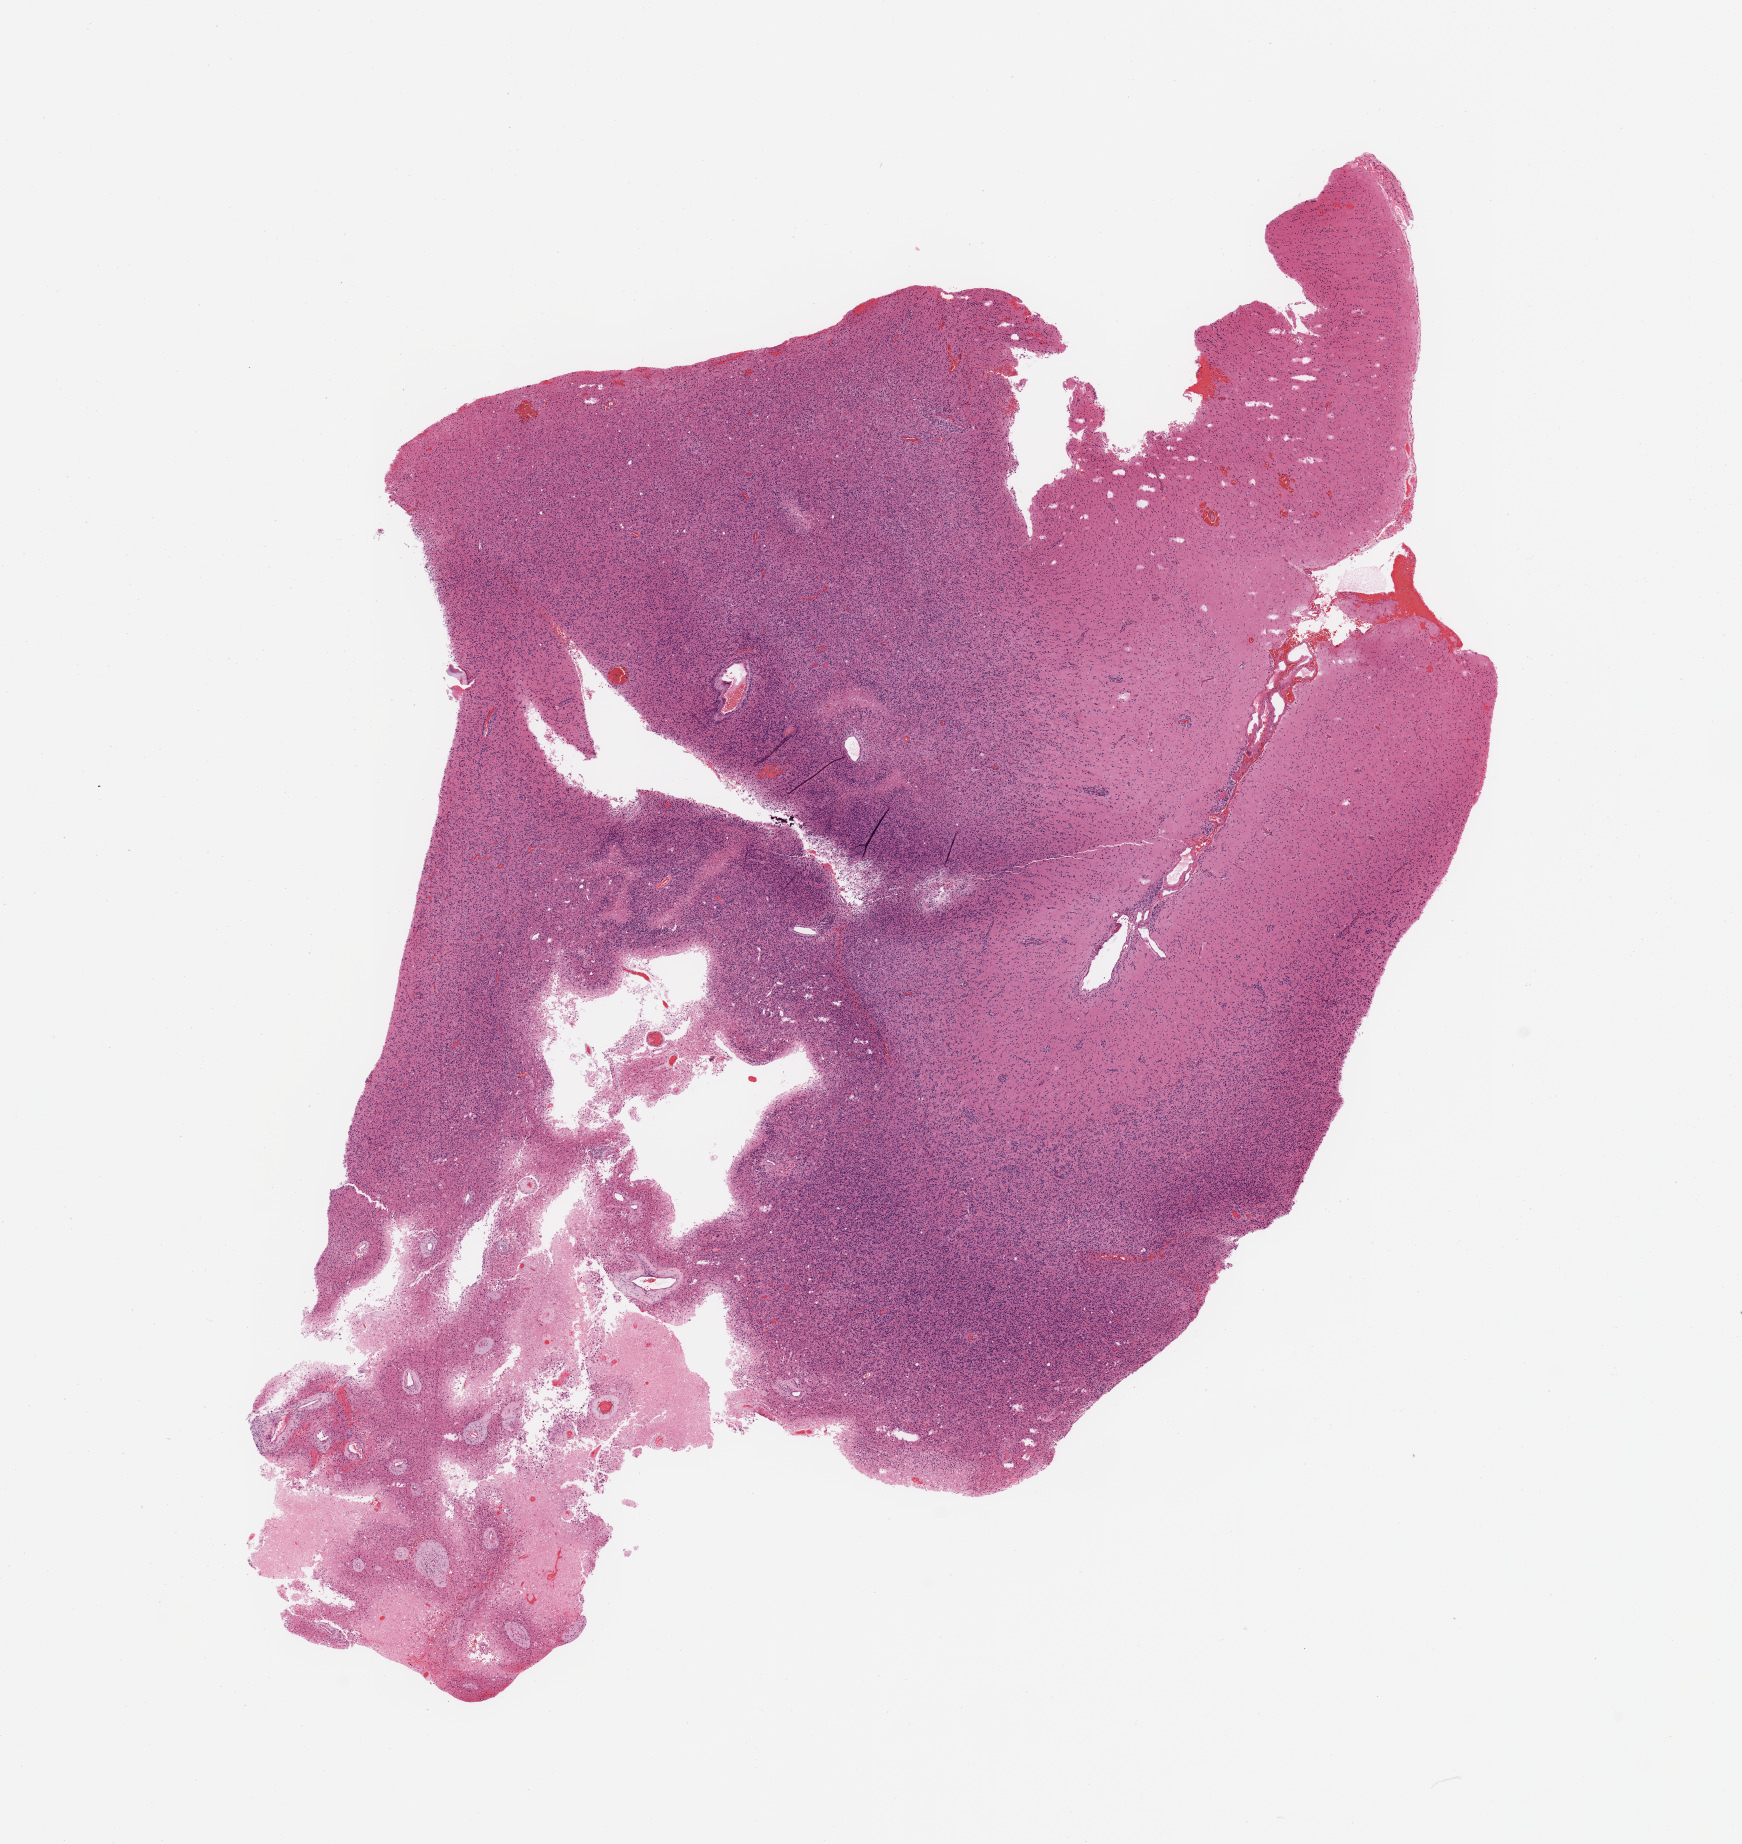
Digitized H&E-stained tissue section (whole slide), low-resolution overview of the scanned area, about 13.8 x 14.6 mm, tumour tissue sample, brain. 70-year-old male patient.
Patient diagnosis (cohort enrolment): glioblastoma multiforme (brain).